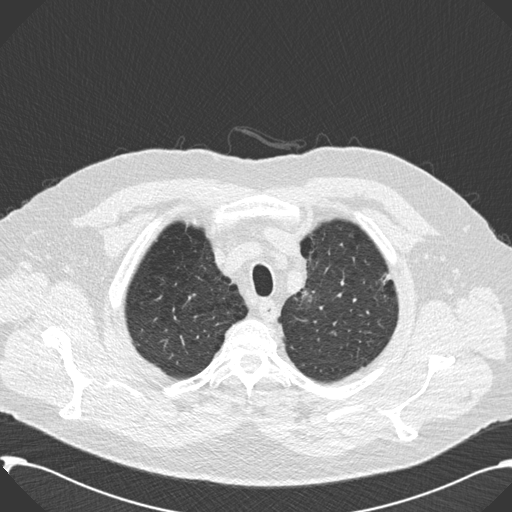
Axial slice from a low-dose chest CT screening exam, second screening round (one year after baseline), lung window (W 1500 / L -600 HU). Male, age 59 years at enrolment. Current smoker at enrolment.
• Expert-annotated lung lesion, bounding box [x1, y1, x2, y2] px = [368, 258, 406, 310].
• No non-calcified nodule or mass ≥4 mm was recorded by the screening reader at this exam.
• Official screen result: negative screen, significant abnormalities not suspicious for lung cancer.
• Lung cancer was diagnosed 518 days after this screen (after the third annual screen): bronchiolo-alveolar carcinoma, mixed mucinous and non-mucinous, left upper lobe, stage IA (AJCC 6th edition), 20 mm at pathology.